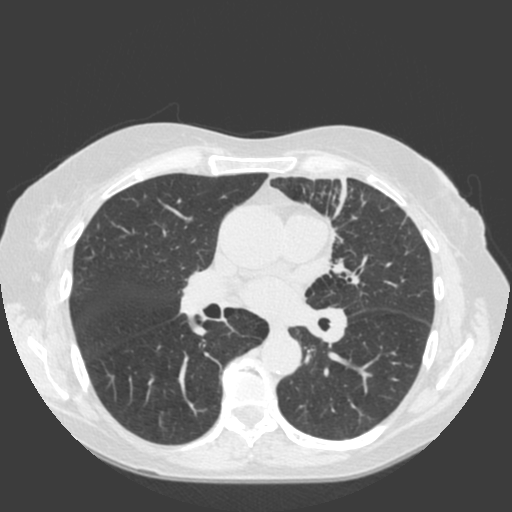
Low-dose screening chest CT, one axial slice; position 104 of 184 along the scan axis; 120 kVp; lung window (W 1500 / L -600 HU); 2 mm slice thickness; 512 × 512 image matrix, field of view 350 × 350 mm.
Structures marked on this image (manually delineated by an expert):
- lesion 1 (tumor, hilum of left lung): box from (x=333, y=259) to (x=349, y=274) px